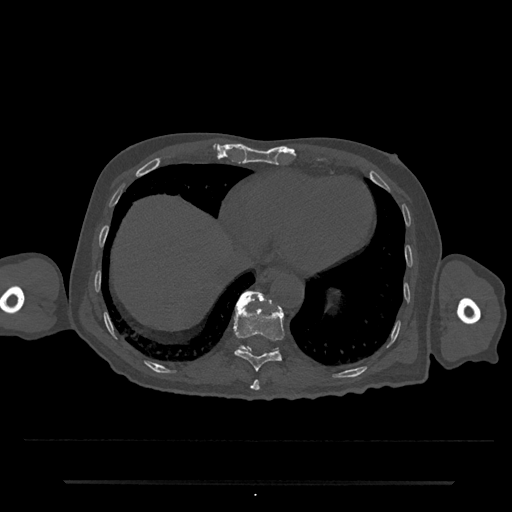
CT including the spine, one axial slice; position 303 of 797 along the scan axis; reconstruction kernel Br40s/3; 120 kVp; bone window (W 1800 / L 400 HU); 512 × 512 image matrix, field of view 427 × 427 mm. Male patient, age 74 years. From the clinical record (not read from this slice): primary cancer: prostate.
Outlined on this slice (semi-automatically segmented with operator editing):
- T10 vertebra: box from (x=233, y=294) to (x=285, y=371) px
- T11 vertebra: (x=236, y=291)–(x=278, y=353)
- T9 vertebra: (x=250, y=380)–(x=260, y=391)